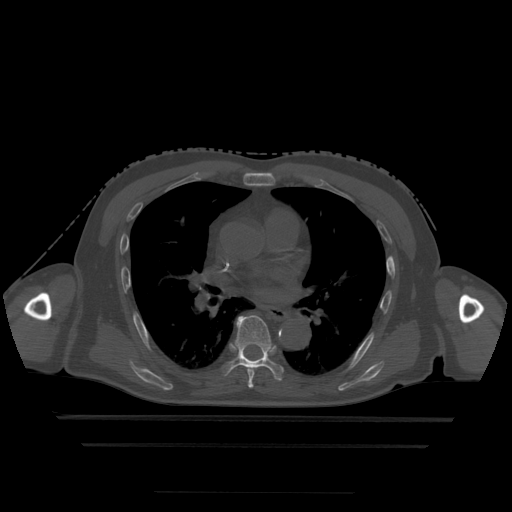
CT including the spine, one axial slice; slice 303 of 522 in the series (ordered by position); bone window (W 1800 / L 400 HU); 1.25 mm slice thickness; 512 × 512 image matrix, field of view 436 × 436 mm. Patient age 68 years. From the clinical record (not read from this slice): primary cancer: urothelial.
Outlined on this slice (semi-automatic segmentation, software-assisted and operator-edited):
- T5 vertebra: bounding box [x1, y1, x2, y2] px = [248, 379, 254, 388]
- T6 vertebra: [246, 367, 255, 381]
- T7 vertebra: [221, 316, 284, 380]